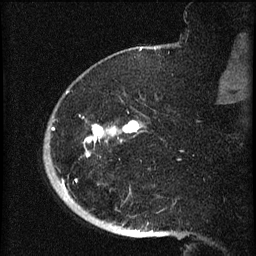
Breast MRI (dynamic contrast-enhanced), one sagittal slice. Position 15 of 60 along the scan axis. Dynamic contrast-enhanced series, image 2 of 3 at this slice position (ordered by acquisition). 1.5 T. TE 4.2 ms, TR 8.2 ms. 2 mm slice thickness. 256 × 256 image matrix, field of view 180 × 180 mm. Female patient, age 71 years.
Annotated regions visible in this slice (semi-automatically segmented with operator editing):
- analysis volume of interest (the breast-tissue region the enhancement analysis was run in; not a lesion): bounding box <44,72,146,196> (left, top, right, bottom; pixels)
- tumour enhancement mask (voxels above the 70 % enhancement threshold inside the analysis volume of interest): <52,121,140,188>